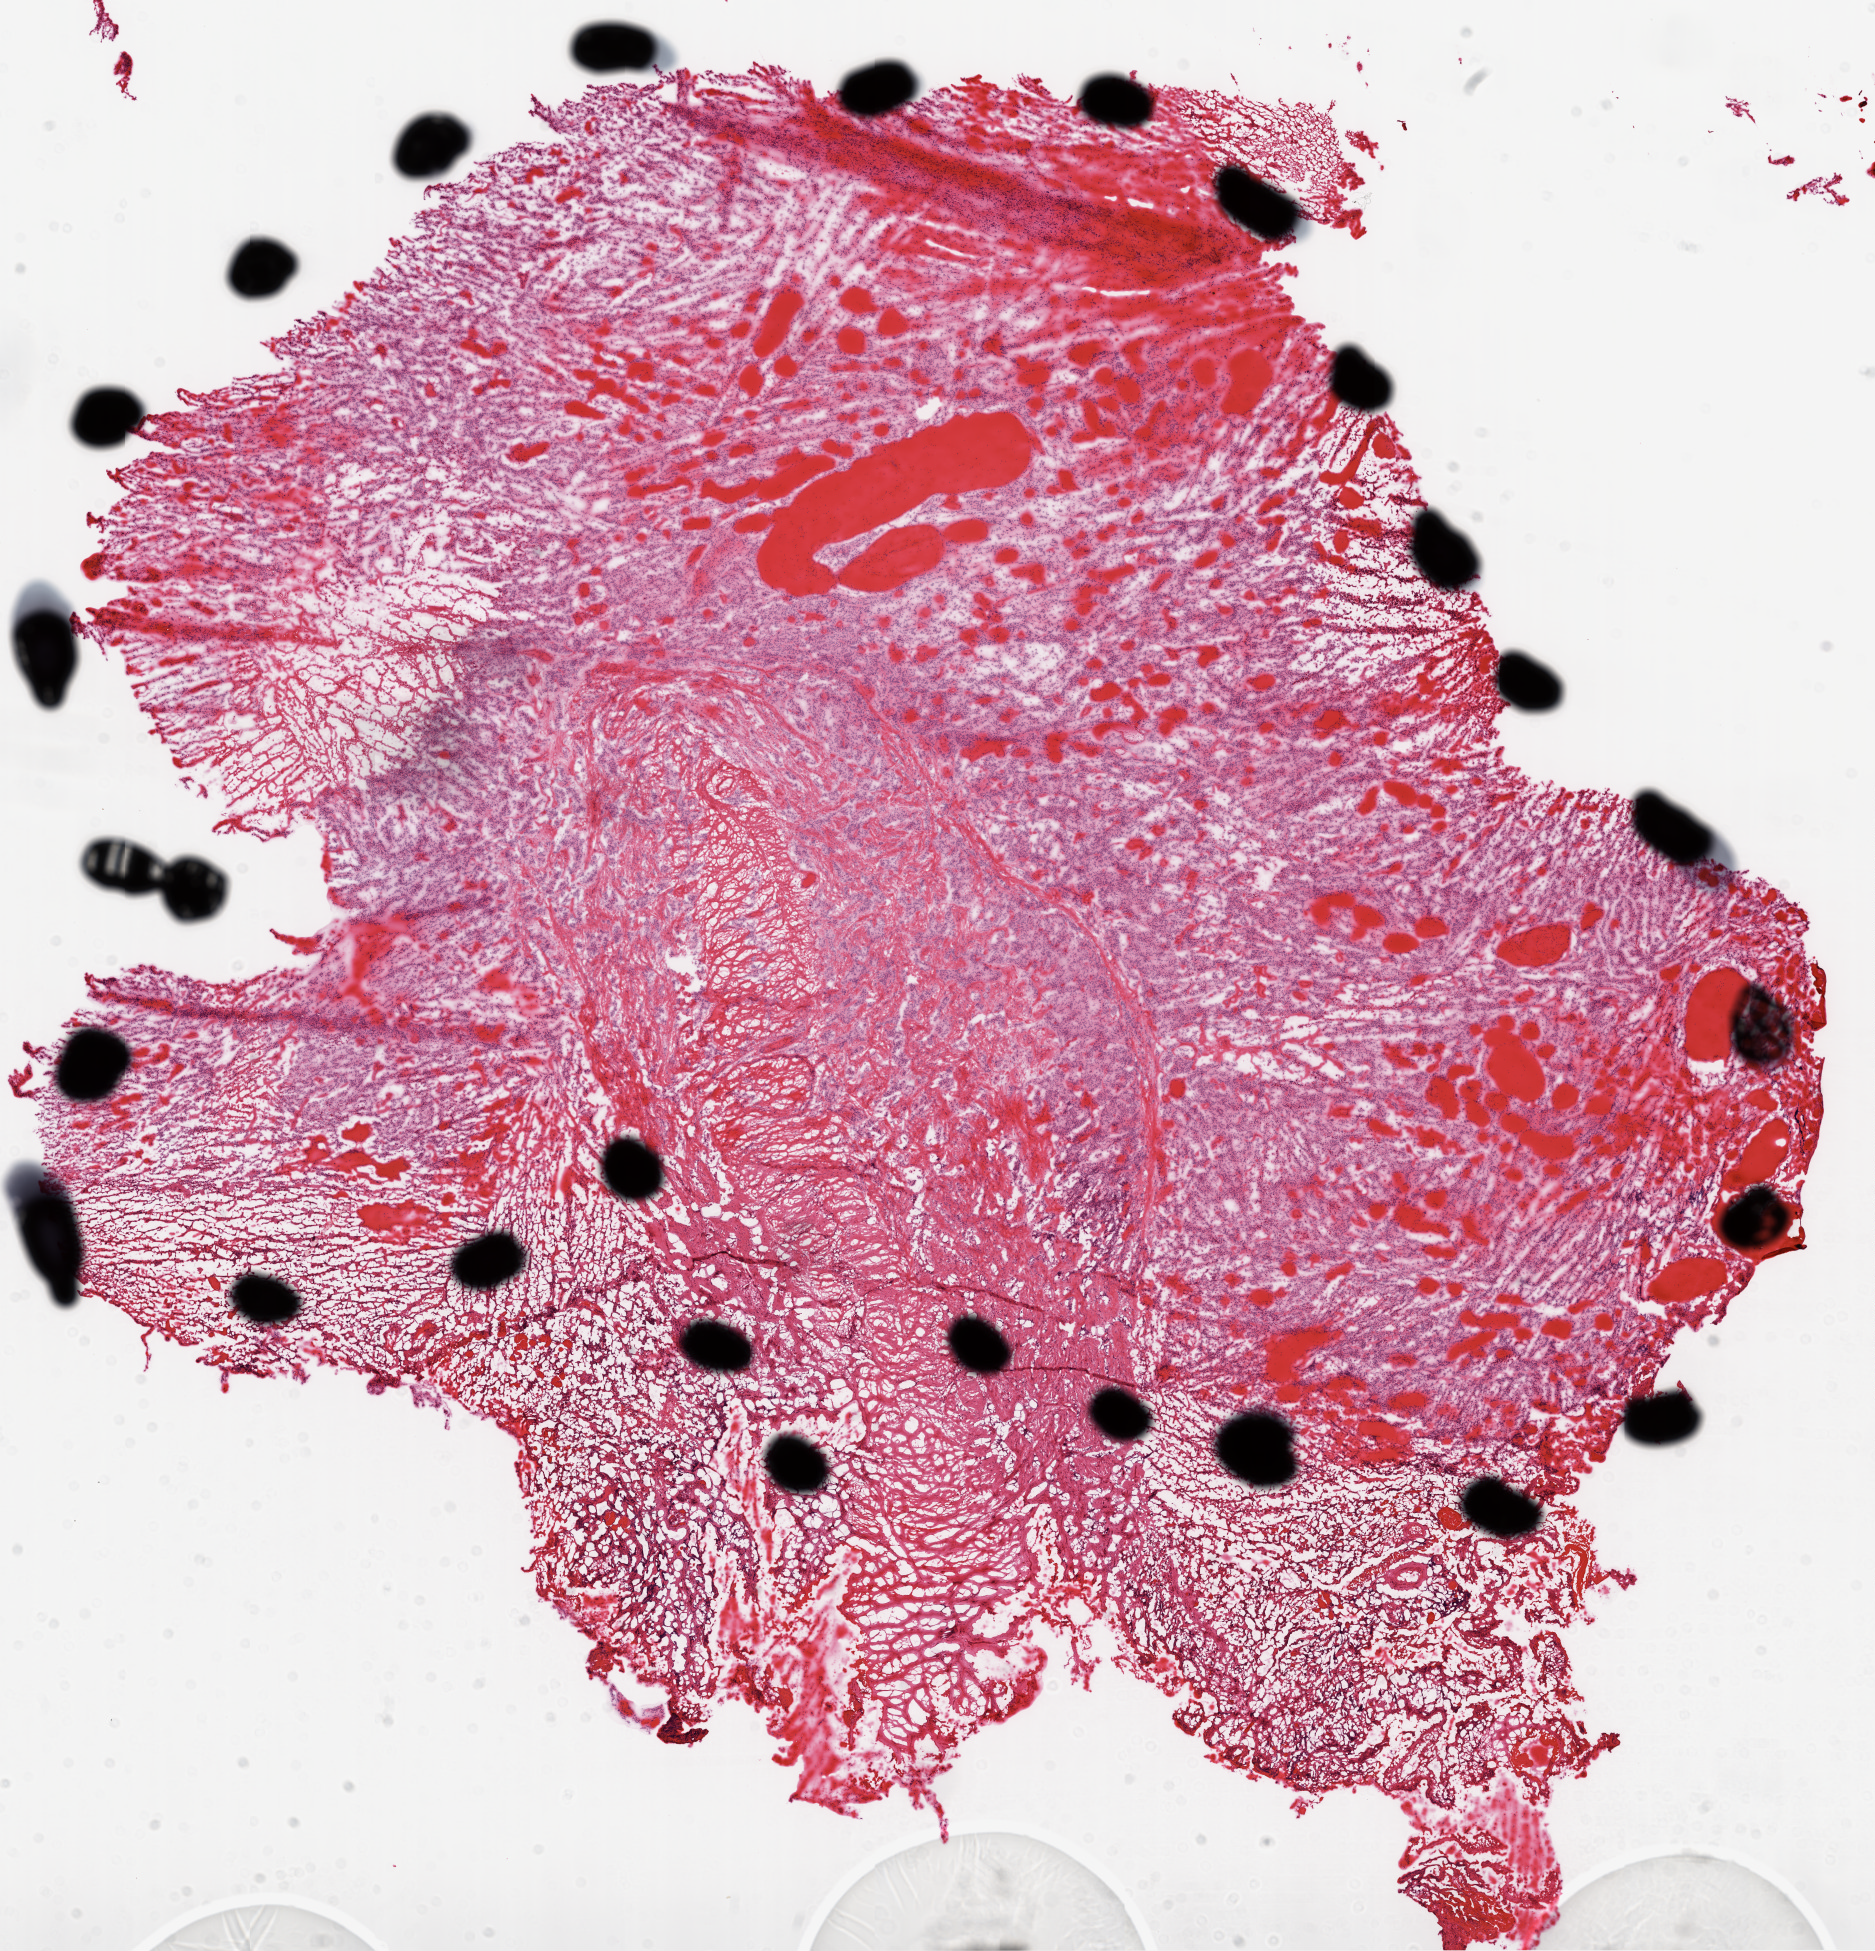
Digitized H&E tissue section (whole slide), a low-resolution overview of the entire scanned area, about 15.0 x 15.7 mm (slide scanned at 20x). Frozen section from the top of the tissue portion. Primary tumour sample from the brain. Female patient; age at initial diagnosis 36 years. Pathologist review of this section (percent, as recorded): tumour cells 90%, tumour nuclei 100%, normal cells 0%, stromal cells 0%, necrosis 10%.
- histologic diagnosis: Glioblastoma